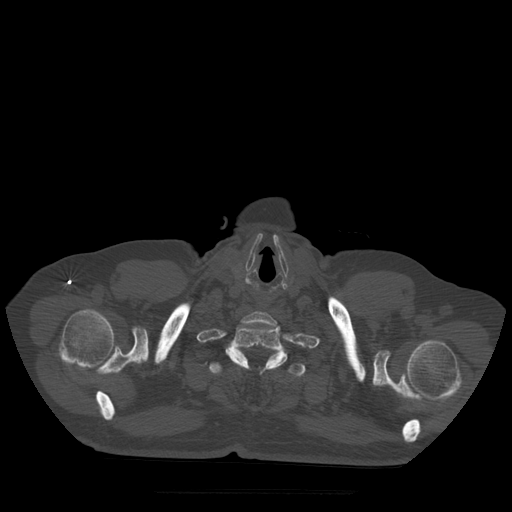
CT including the spine, one axial slice; position 438 of 522 along the scan axis; bone window (W 1800 / L 400 HU); 1.25 mm slice thickness; 512 × 512 image matrix. Patient age 72 years. Case-level facts recorded for this patient, not image findings: primary cancer: prostate.
Annotated regions visible in this slice (semi-automatic segmentation, software-assisted and operator-edited):
- T1 vertebra: bounding box [x1, y1, x2, y2] px = [225, 327, 288, 370]
- T2 vertebra: [209, 362, 306, 377]